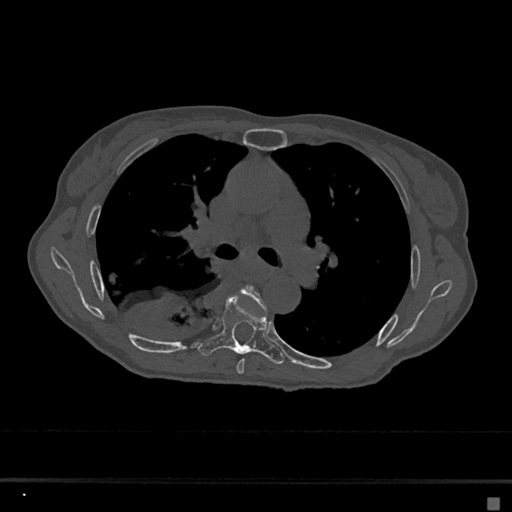
CT including the spine, one axial slice; slice 431 of 797 in the series (ordered by position); bone window (W 1800 / L 400 HU); 0.5 mm slice thickness; 512 × 512 image matrix. Female patient, age 68 years. Case-level facts recorded for this patient, not image findings: primary cancer: renal.
Structures marked on this image (semi-automatic segmentation, software-assisted and operator-edited):
- T5 vertebra: bounding box (x1, y1, x2, y2) in pixels: (230, 285, 267, 375)
- T6 vertebra: (198, 295, 284, 364)